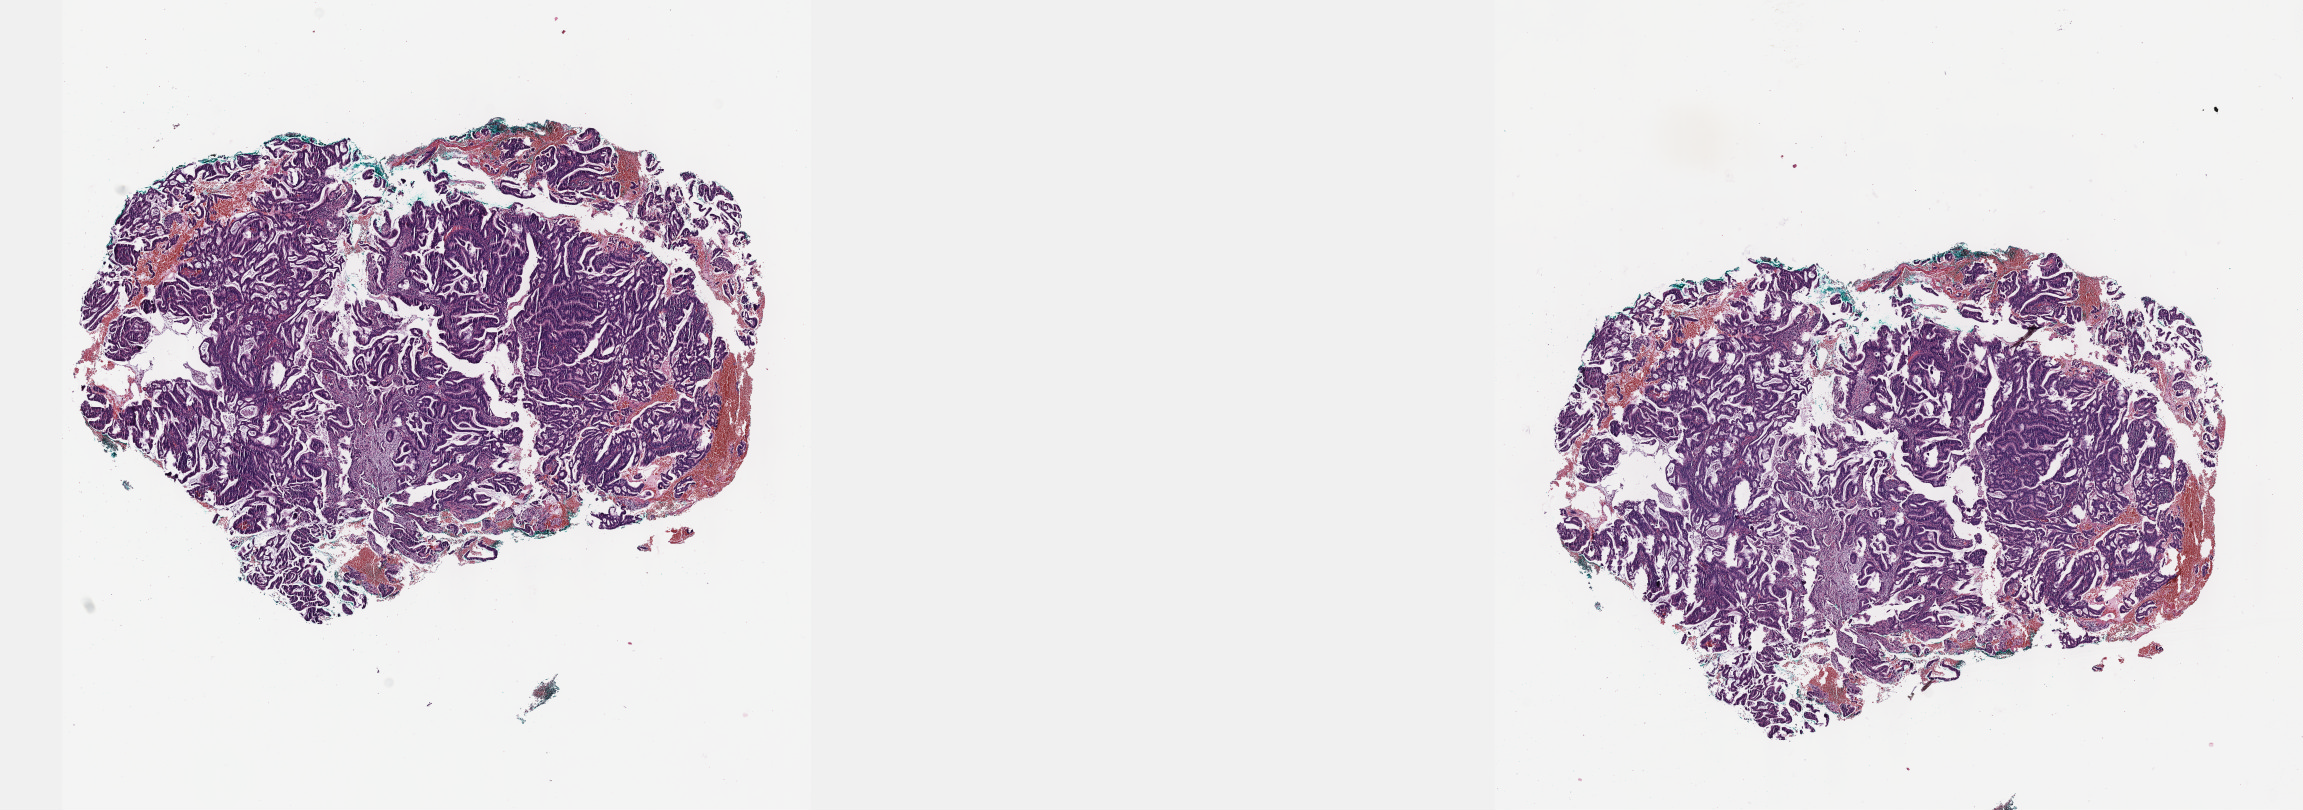
Whole-slide histology image, H&E-stained, shown as a low-resolution overview of the whole scanned area (about 18.6 x 6.5 mm); formalin-fixed paraffin-embedded (FFPE) diagnostic section; primary tumour sample from the cervix. Female, age 66 years at initial diagnosis. Histologic grade: G2 (moderately differentiated).
- diagnosis: Mucinous adenocarcinoma, endocervical type (cervix uteri)
- FIGO stage: IB1
- lymph nodes positive (case pathology): 0 of 15 examined